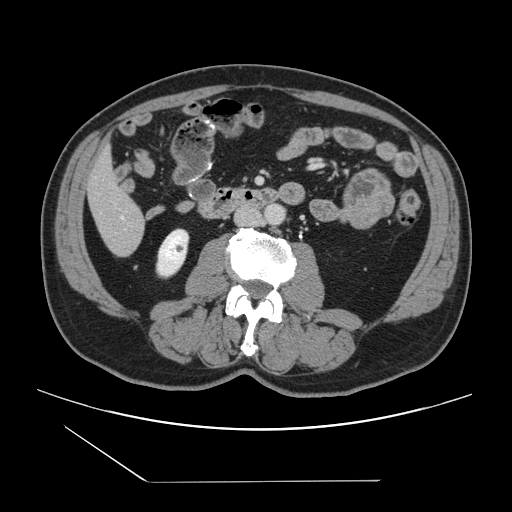
Contrast-enhanced abdominal CT, one axial slice. Slice 28 of 157 in the series (ordered by position). Soft-tissue window (W 400 / L 40 HU). 2.5 mm slice thickness. 512 × 512 image matrix, field of view 407 × 407 mm. Male patient, age 61 years. From the clinical record (not read from this slice): diagnosis: colorectal cancer liver metastases, imaged before liver resection; multiple liver metastases: yes; largest metastasis: 5.5 cm; disease in both lobes: yes.
Outlined on this slice (manually delineated by an expert):
- hepatic veins: bounding box (x1, y1, x2, y2) in pixels: (121, 216, 124, 218)
- liver: (89, 153, 145, 256)
- planned liver remnant (the part of the liver to remain after resection): (88, 153, 139, 218)